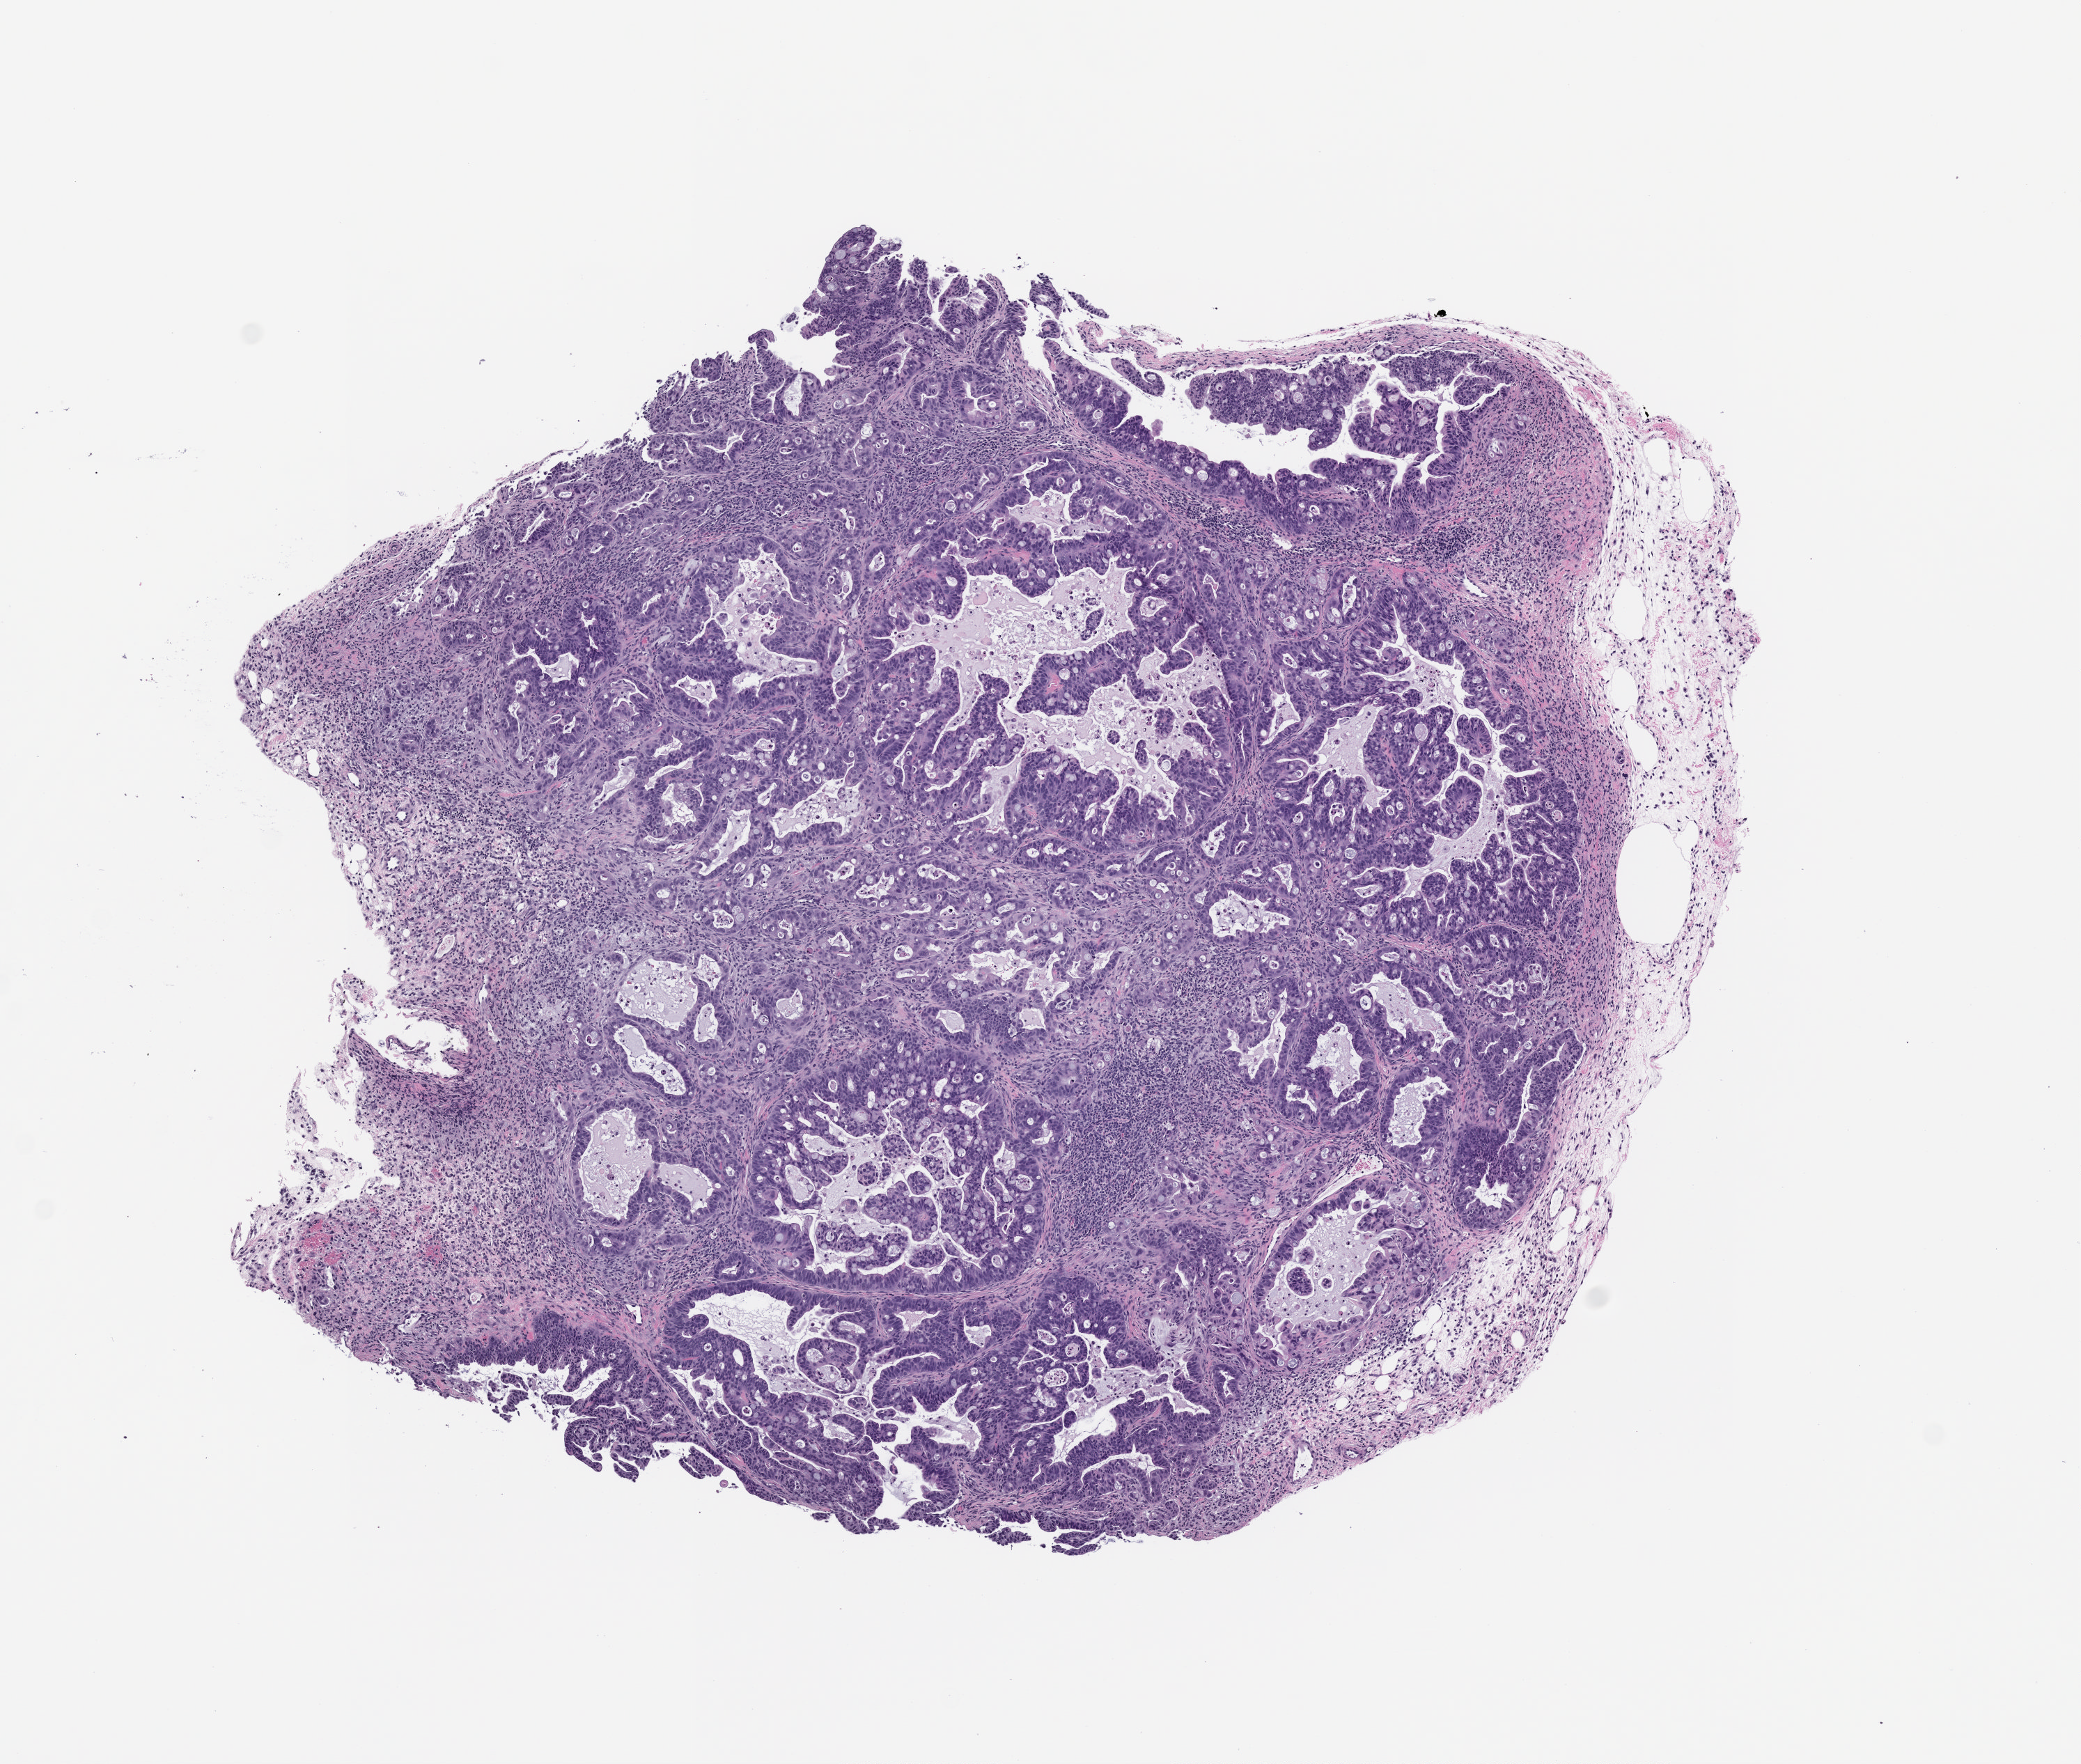
Haematoxylin and eosin whole-slide image of a patient-derived xenograft (PDX) tumor grown in a mouse — shown as a low-resolution overview of the whole scanned area (about 6.0 x 5.1 mm); FFPE section; tumor site category: small intestine.
• originating patient diagnosis: Small Intestinal Adenocarcinoma